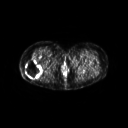
FDG PET of an extremity soft-tissue mass (from a PET/CT study), one axial slice. Position 32 of 267 along the scan axis. 128 × 128 image matrix. Female patient, age 57 years. Case-level facts recorded for this patient, not image findings: histological type: epithelioid sarcoma with vascular differentiation; site of the primary tumour: right buttock.
Structures marked on this image (expert contour drawn on MRI and transferred to this co-registered scan by the dataset authors):
- gross tumour volume (mass): box from (x=24, y=59) to (x=43, y=78) px